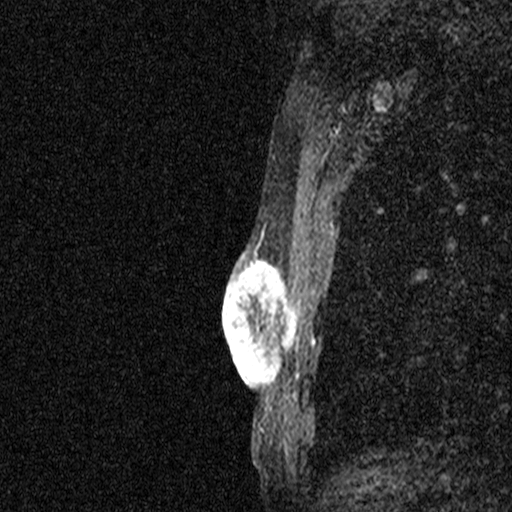
Breast MRI (dynamic contrast-enhanced), one sagittal slice; position 32 of 44 along the scan axis; dynamic contrast-enhanced study with each time point stored as its own series, time point 2 of 3 at this slice position (early post-contrast, ordered by acquisition time); 1.5 T; TE 4.5 ms, TR 11 ms; 2.05 mm slice thickness; 512 × 512 image matrix, field of view 200 × 200 mm. Female patient, age 44 years. Case-level facts recorded for this patient, not image findings: setting: breast cancer imaged before/during neoadjuvant chemotherapy; receptor status: HR-positive, HER2-negative.
Structures marked on this image (semi-automatically segmented with operator editing):
- analysis volume of interest (the breast-tissue region the enhancement analysis was run in; not a lesion): bounding box <204,254,300,401> (left, top, right, bottom; pixels)
- tumour enhancement mask (voxels above the 90 % enhancement threshold inside the analysis volume of interest): <222,254,299,401>